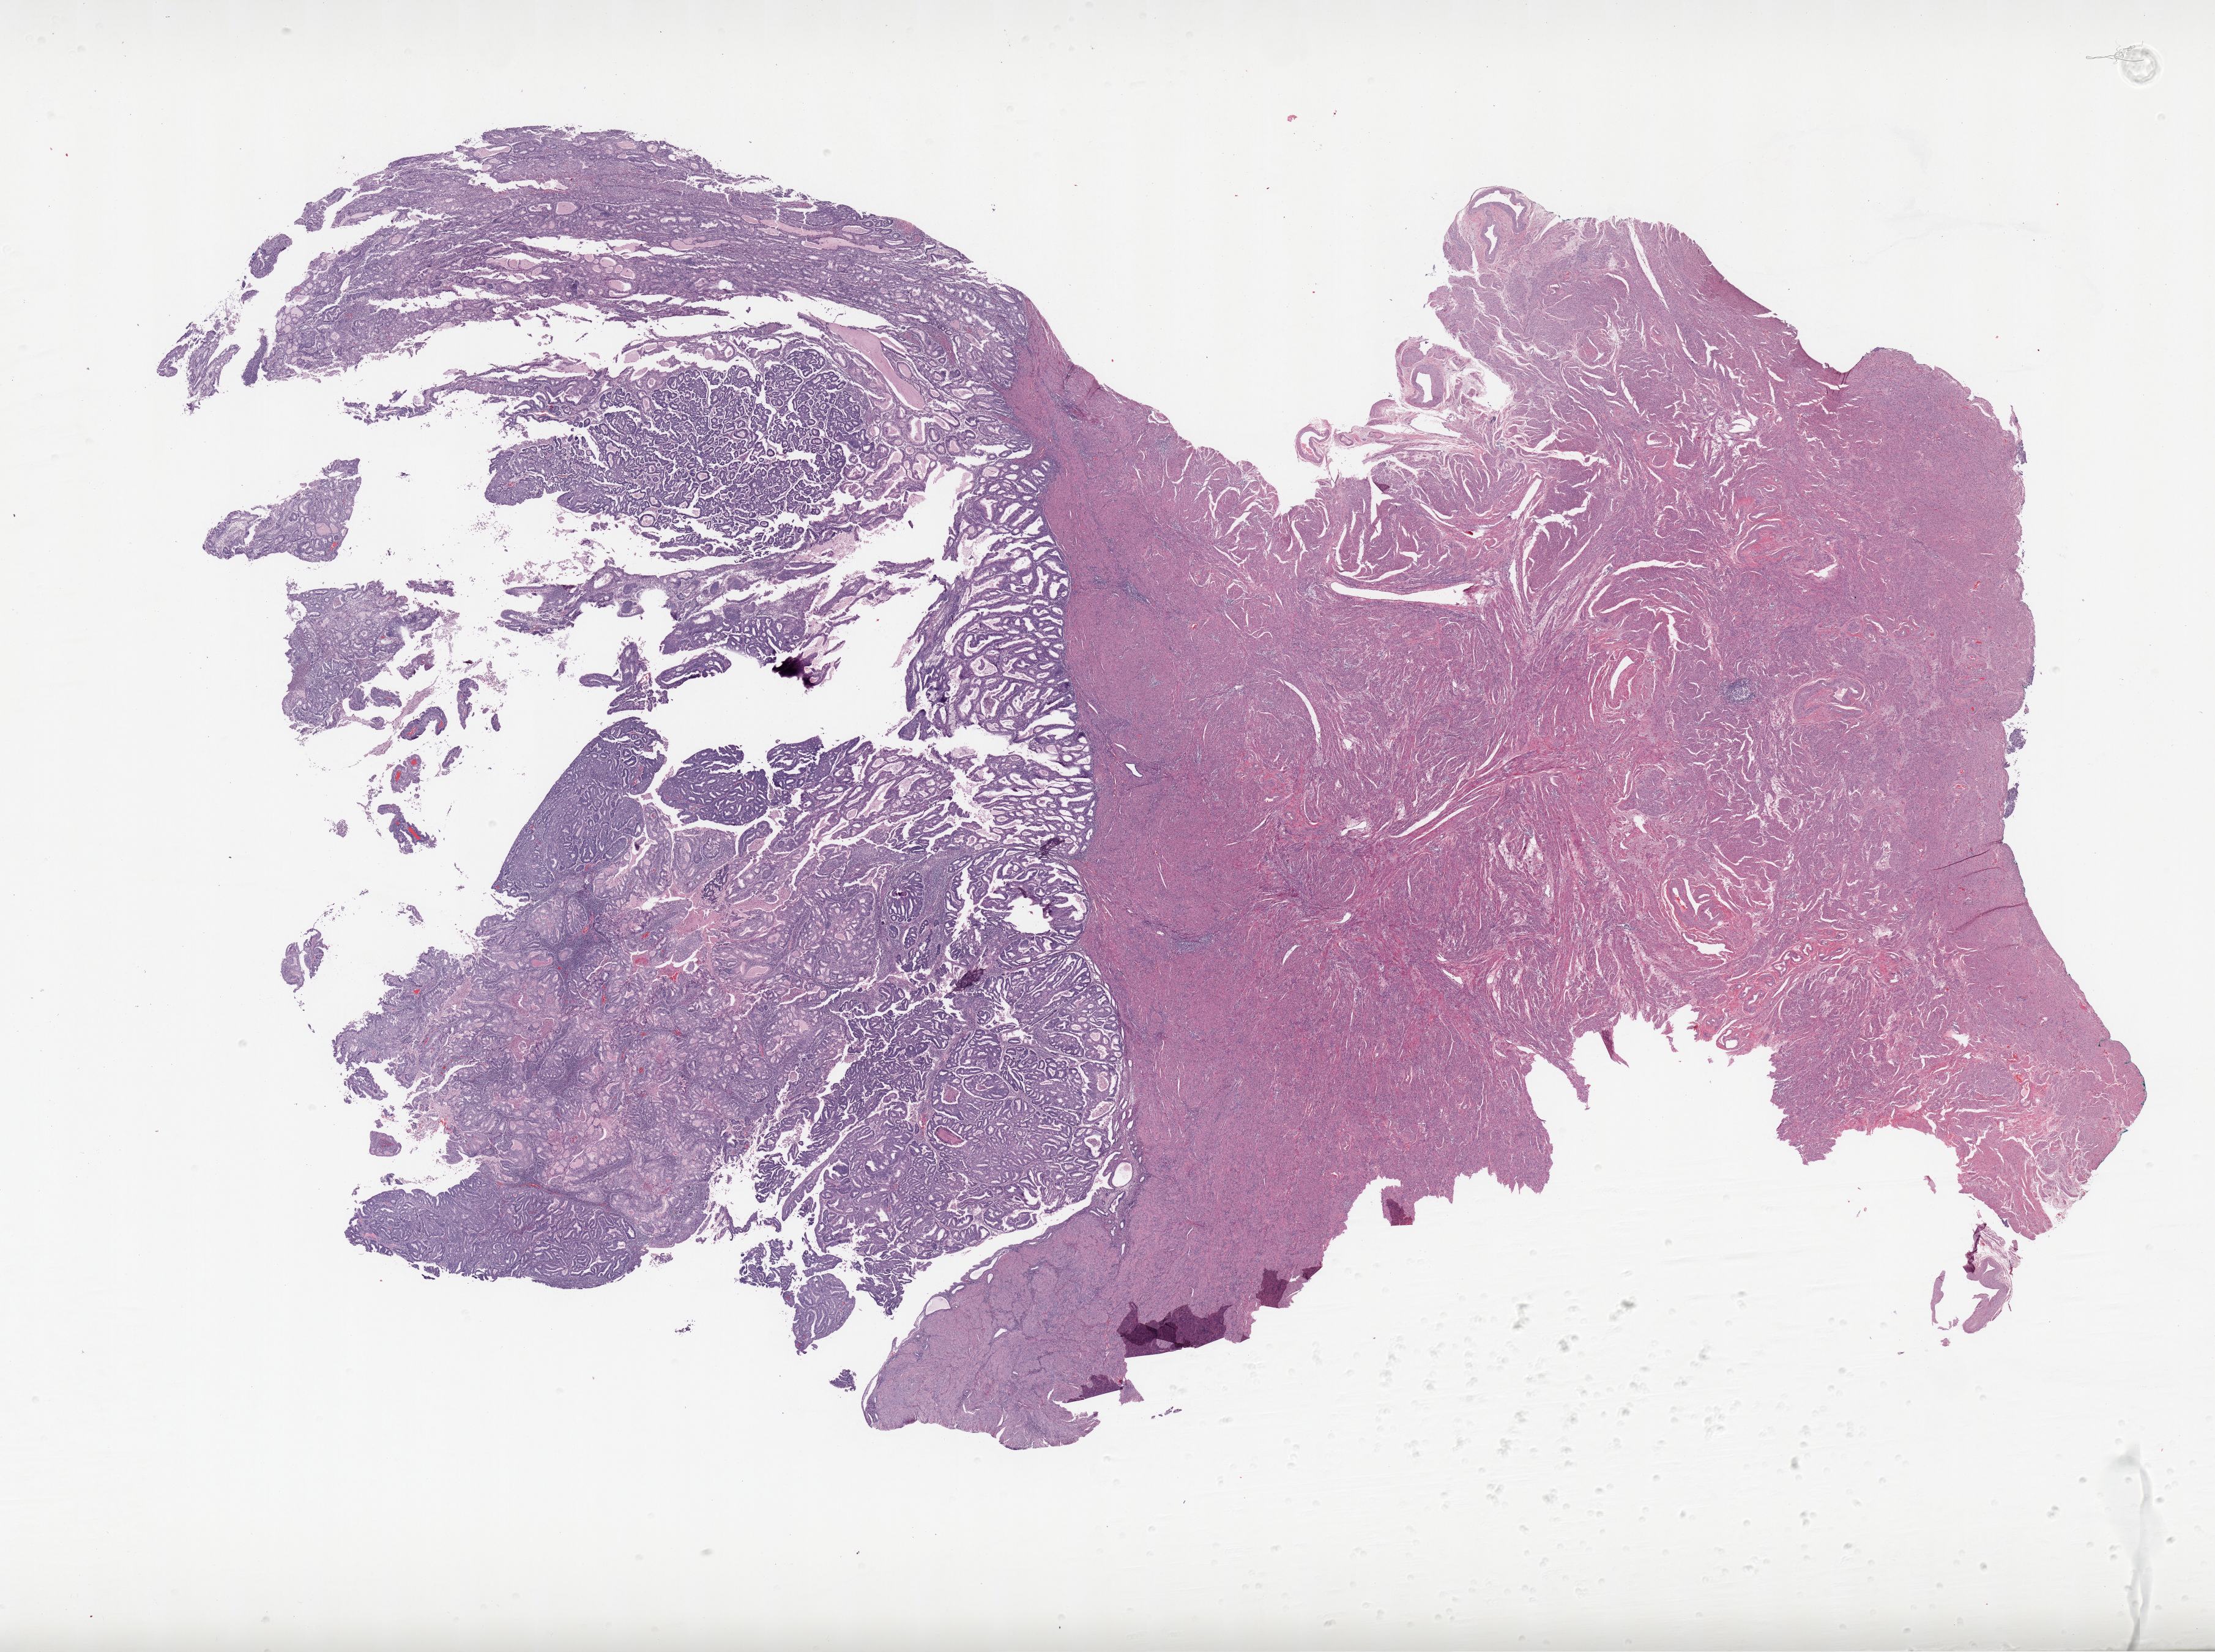
Digitized H&E-stained tissue section (whole slide), whole scanned area (about 28.8 x 21.5 mm, from a 20x scan) shown as a low-resolution overview; formalin-fixed paraffin-embedded (FFPE) diagnostic section; primary tumour sample from the uterus. Female patient; age at initial diagnosis 62 years. Histologic grade: G3 (poorly differentiated).
FIGO stage: IA. Diagnosis: Endometrioid adenocarcinoma, NOS (endometrium).